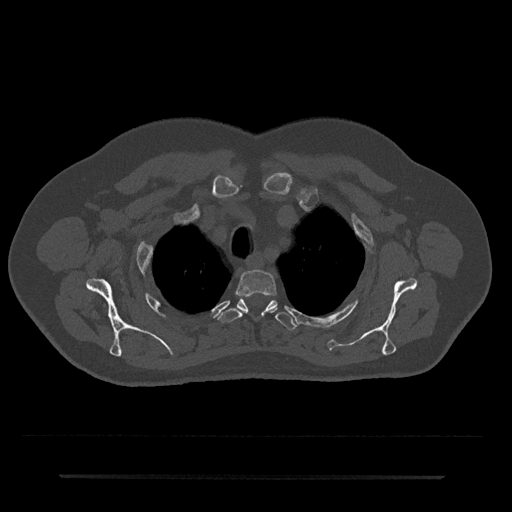
CT including the spine, one axial slice; slice 584 of 797 in the series (ordered by position); 120 kVp; bone window (W 1800 / L 400 HU); 0.5 mm slice thickness; 512 × 512 image matrix. Male patient, age 69 years. From the clinical record (not read from this slice): primary cancer: prostate.
Structures marked on this image (semi-automatically segmented with operator editing):
- T2 vertebra: box from (x=235, y=269) to (x=276, y=297) px
- T3 vertebra: (x=218, y=298)–(x=298, y=330)